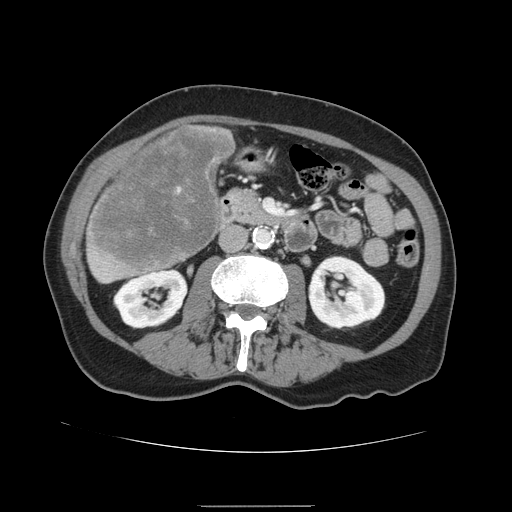
Contrast-enhanced abdominal CT, one axial slice. Position 45 of 168 along the scan axis. Soft-tissue window (W 400 / L 40 HU). 2.5 mm slice thickness. 512 × 512 image matrix, field of view 386 × 386 mm. Male patient, age 74 years. From the clinical record (not read from this slice): diagnosis: colorectal cancer liver metastases, imaged before liver resection; multiple liver metastases: no; largest metastasis: 14.5 cm; chemotherapy before resection: no.
Structures marked on this image (outlined manually by an expert reader):
- liver: bounding box [x1, y1, x2, y2] px = [85, 124, 235, 284]
- liver metastasis: [89, 127, 234, 270]